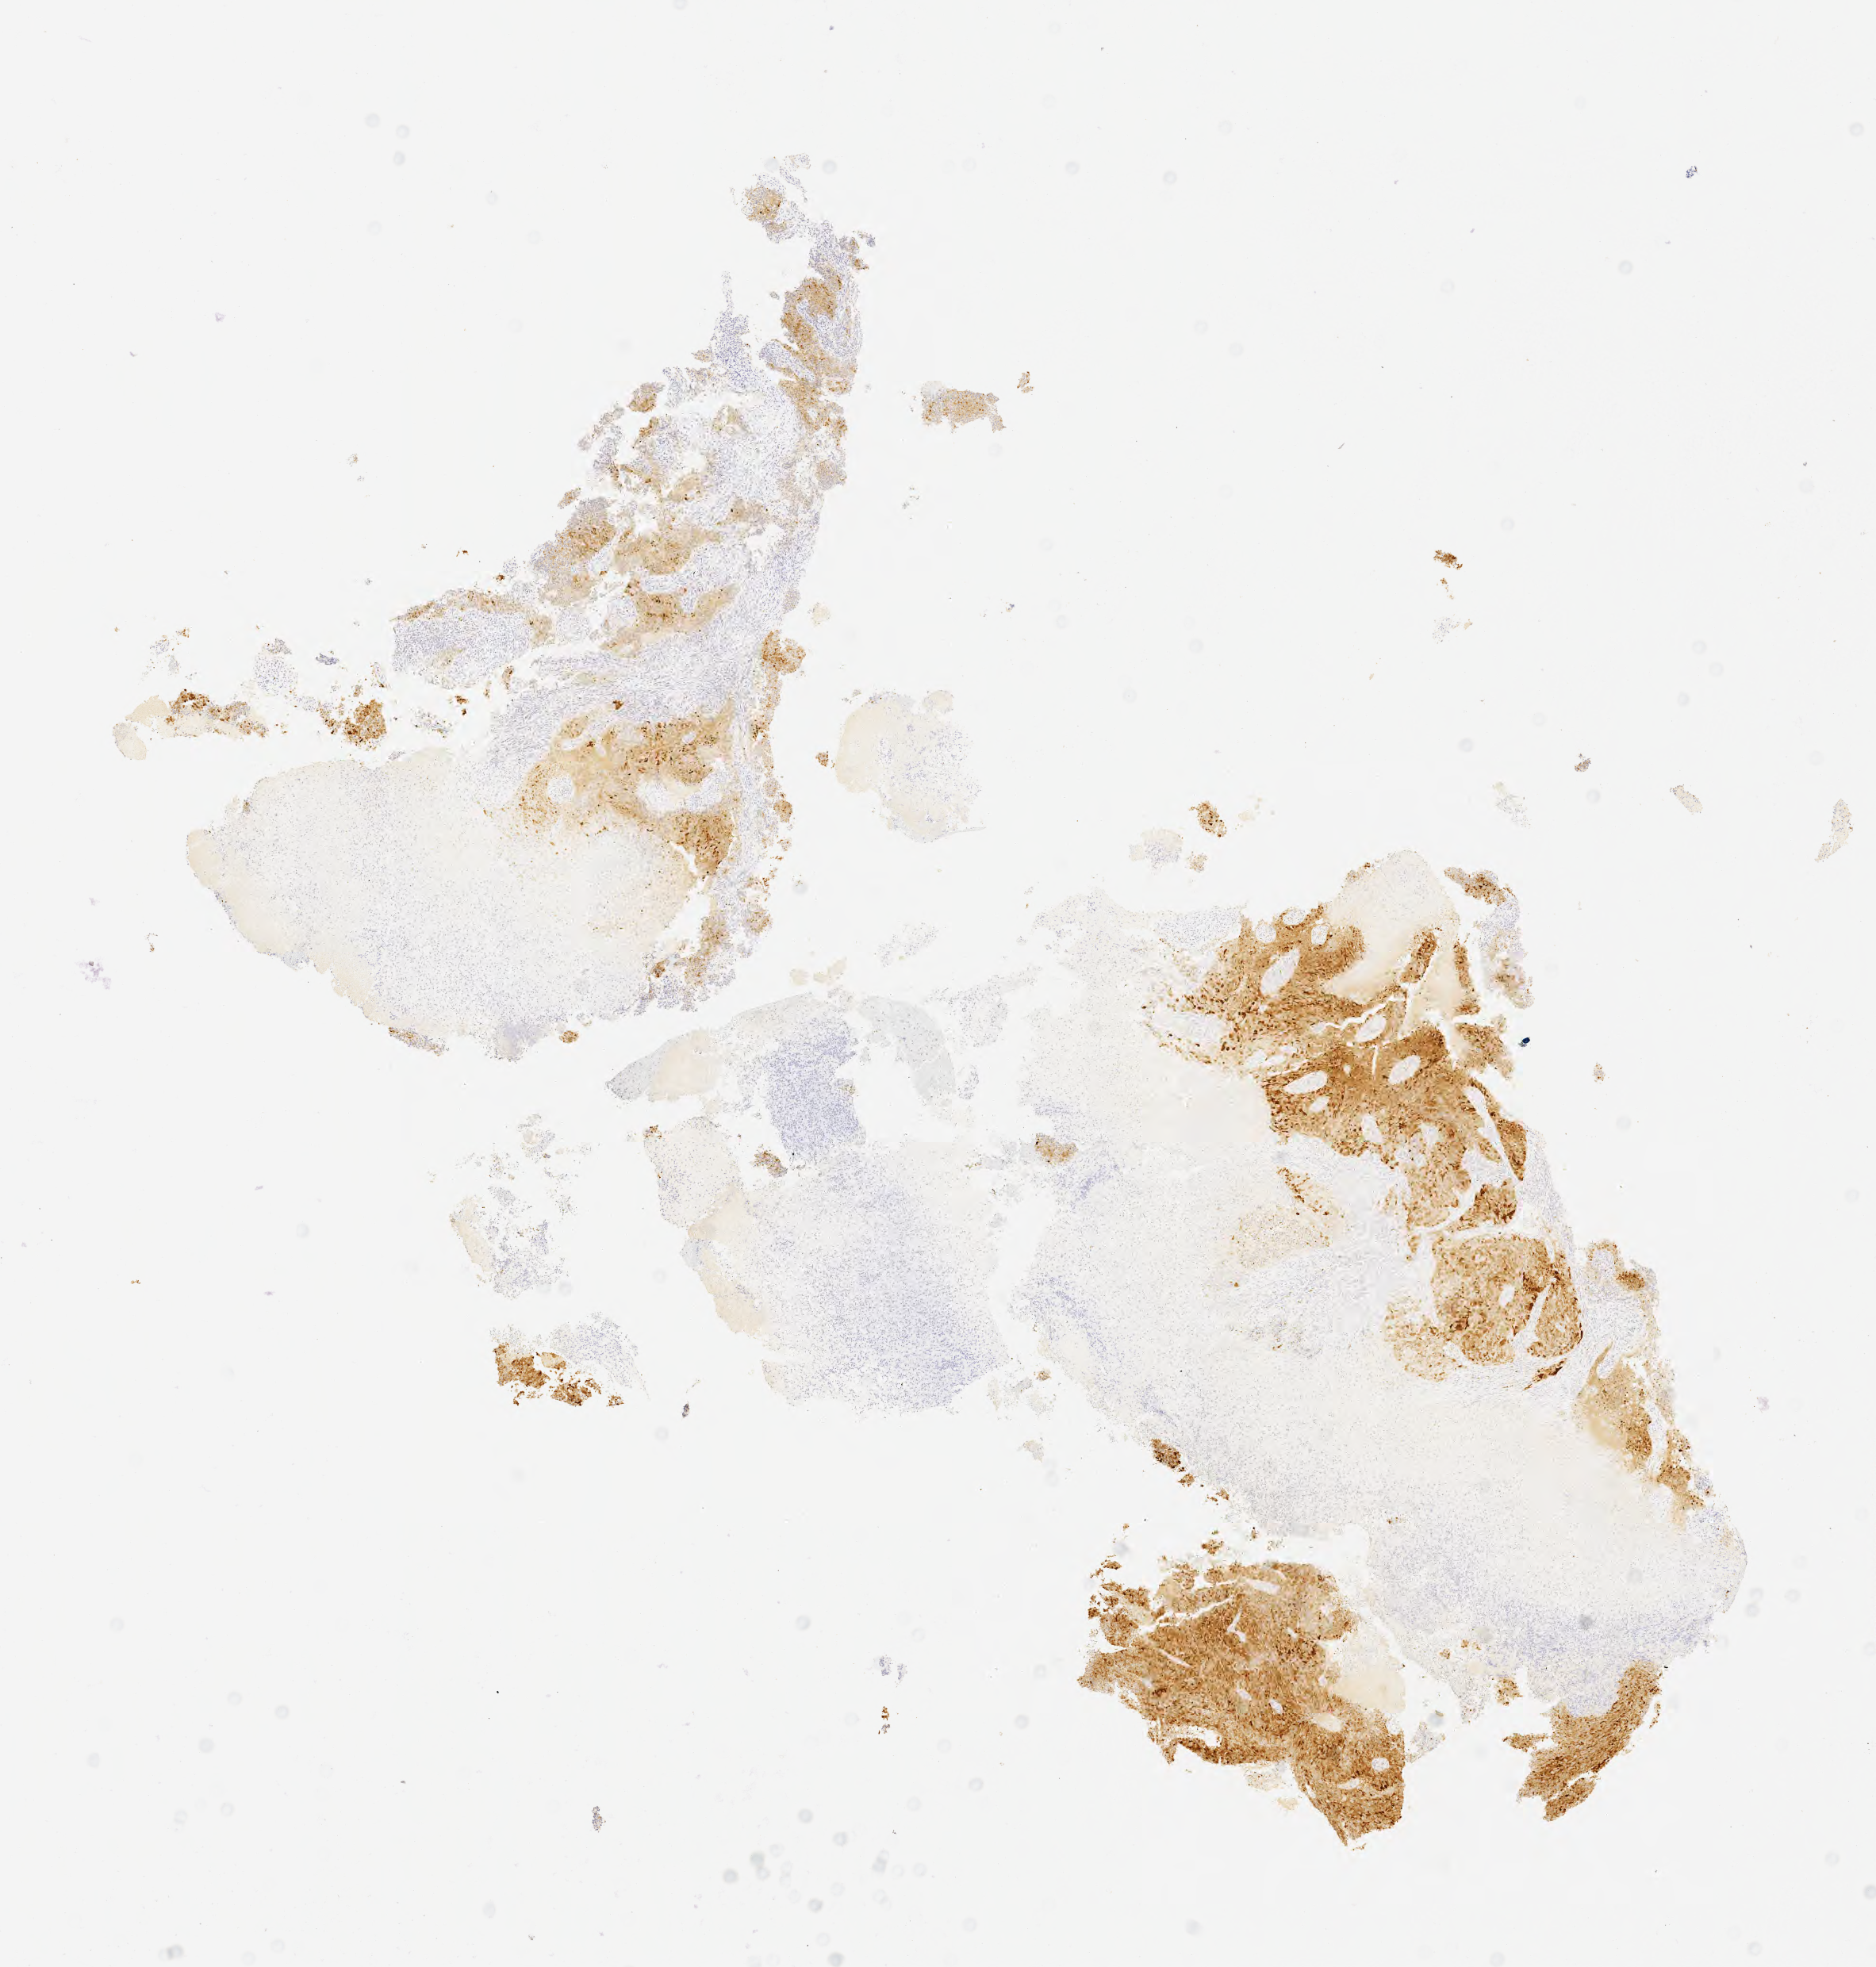
Whole-slide image, immunohistochemical stain for p16 (p16INK4a) — a low-resolution overview of the entire scanned area, about 9.6 x 10.0 mm; specimen: tumor tissue; site: cervix. Patient: female, 65 years old.
Histologic diagnosis: Squamous cell carcinoma, large cell, nonkeratinizing, NOS.